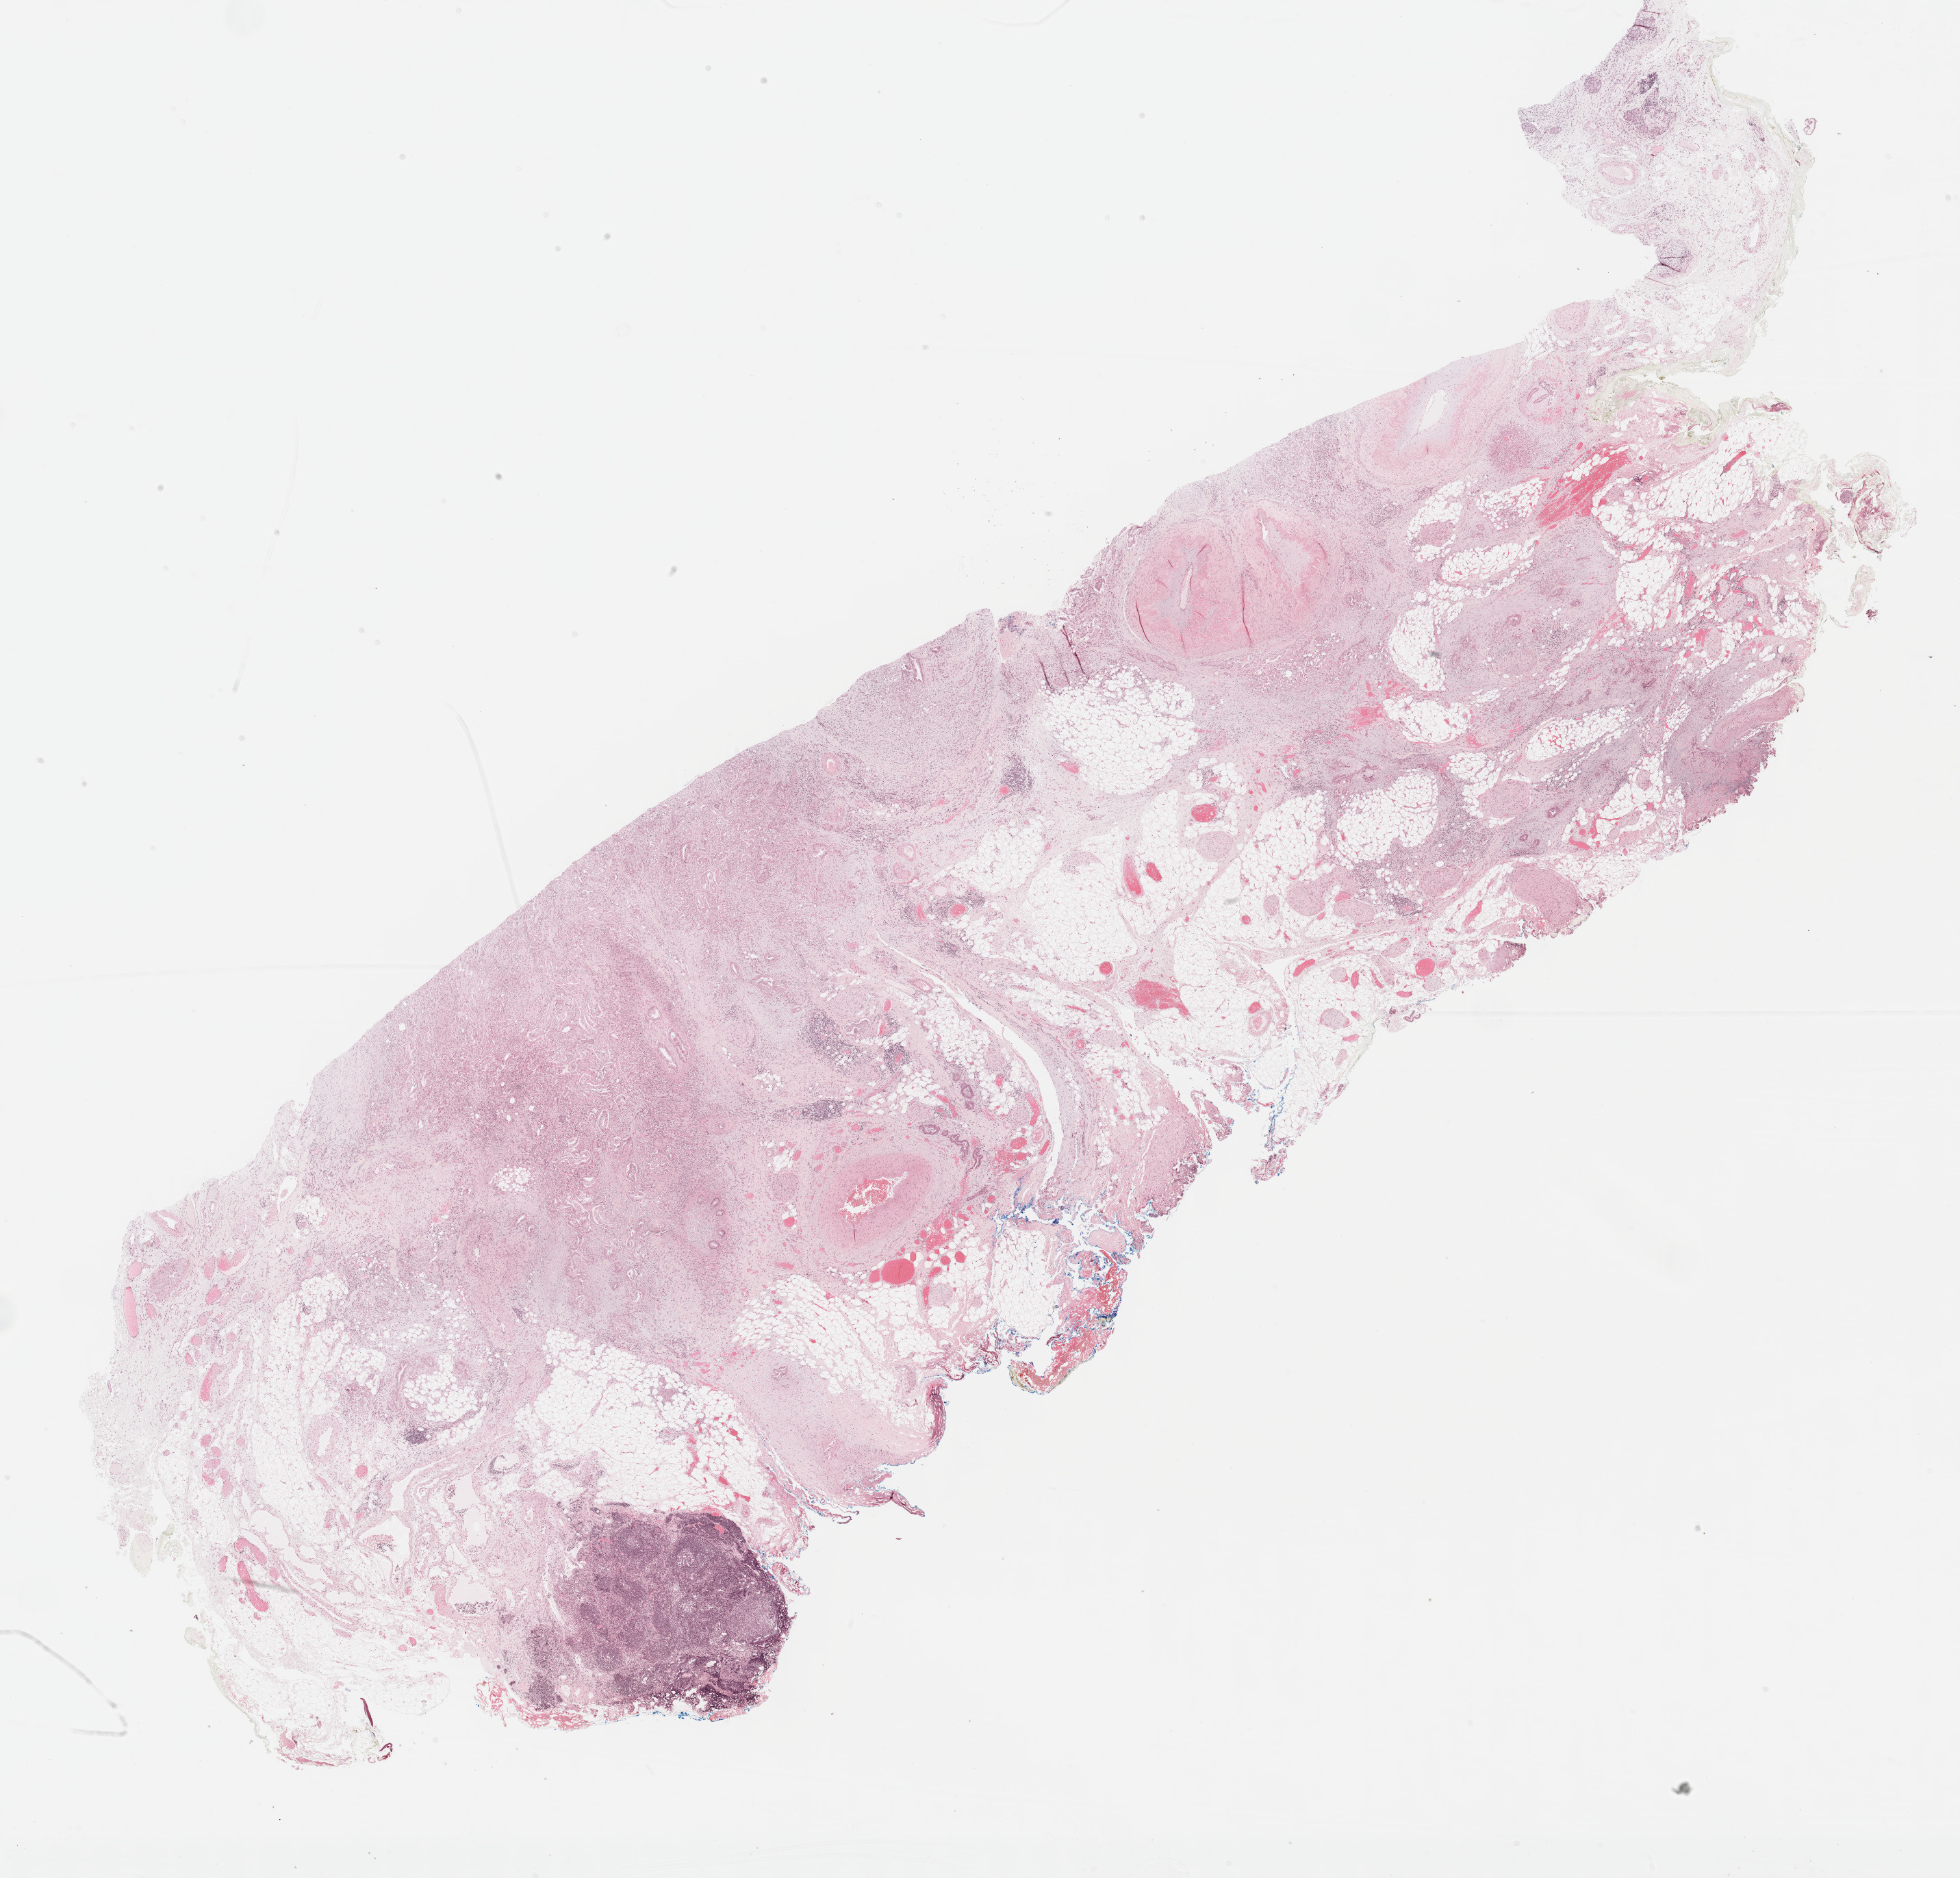
Whole-slide histology image, Hematoxylin and eosin (H&E) stained — a low-resolution overview of the entire scanned area, about 23.2 x 22.2 mm (from a 40x scan); formalin-fixed paraffin-embedded (FFPE) diagnostic section; pancreas, primary tumour sample. Female, age 78 years at initial diagnosis. Histologic grade: G2 (moderately differentiated).
* pathologic diagnosis: Infiltrating duct carcinoma, NOS
* AJCC pathologic stage: IIB (7th edition)
* lymph nodes positive (case pathology): 3 of 12 examined